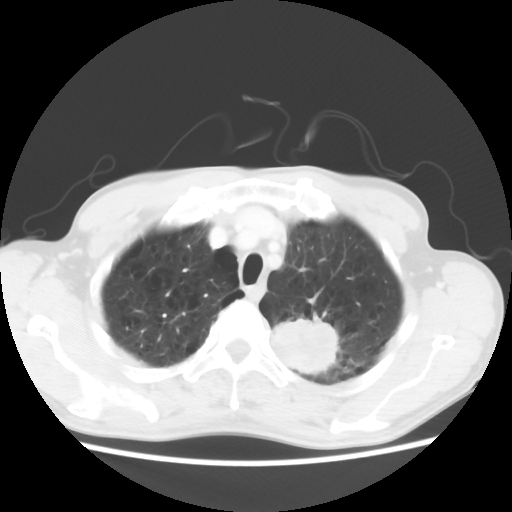
Chest CT, one axial slice; slice 53 of 64 in the series (ordered by position); reconstruction kernel STANDARD; 120 kVp; lung window (W 1500 / L -600 HU); 5 mm slice thickness; 512 × 512 image matrix, field of view 346 × 346 mm. Patient: male, 63 years. Case-level facts recorded for this patient, not image findings: clinical TNM (as recorded): T2 N0 M0.
Annotated regions visible in this slice (bounding box drawn by a radiologist):
- lung tumour (recorded histology: adenocarcinoma): bounding box [x1, y1, x2, y2] px = [269, 312, 341, 377]